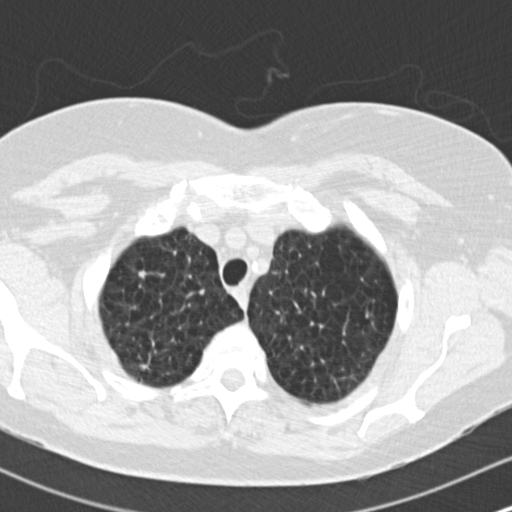
Chest CT (low-dose screening protocol), one axial image; baseline annual screen; lung window (W 1500 / L -600 HU); 2 mm slice thickness; standard (soft-tissue) reconstruction kernel (B30f); slice 24 of 172 in the series; 512 × 512 image matrix, field of view 310 × 310 mm. Female participant, aged 73 years at enrolment. Former smoker at enrolment.
Expert-annotated lung lesion, bounding box [x1, y1, x2, y2] px = [125, 251, 175, 292]. The screening reader recorded 2 non-calcified nodules or masses ≥4 mm on this exam (right upper lobe, right upper lobe); which of them this box marks is not recorded. Official screen result: positive, change unspecified: nodule(s) >= 4 mm or enlarging nodule(s), mass(es), or other non-specific abnormalities suspicious for lung cancer. Lung cancer was diagnosed 601 days after this screen (after the second annual screen): adenocarcinoma, NOS, right upper lobe, moderately differentiated (G2), stage IB (AJCC 6th edition), 15 mm at pathology.